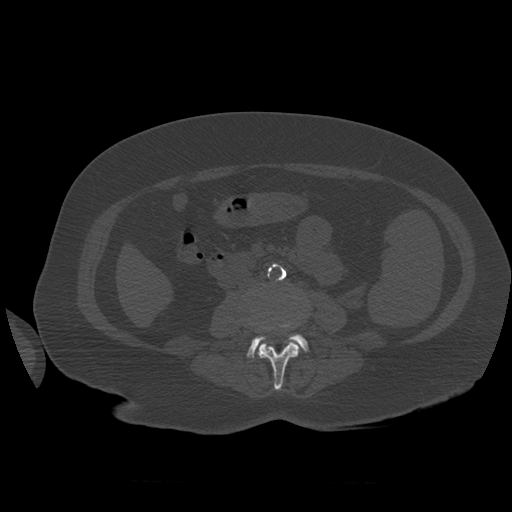
CT including the spine, one axial slice; slice 220 of 399 in the series (ordered by position); 120 kVp; bone window (W 1800 / L 400 HU); 1.25 mm slice thickness; 512 × 512 image matrix. Patient age 81 years. Case-level facts recorded for this patient, not image findings: primary cancer: renal.
Structures marked on this image (semi-automatically segmented with operator editing):
- L3 vertebra: bounding box (x1, y1, x2, y2) in pixels: (258, 323, 300, 391)
- L4 vertebra: (247, 325, 308, 358)